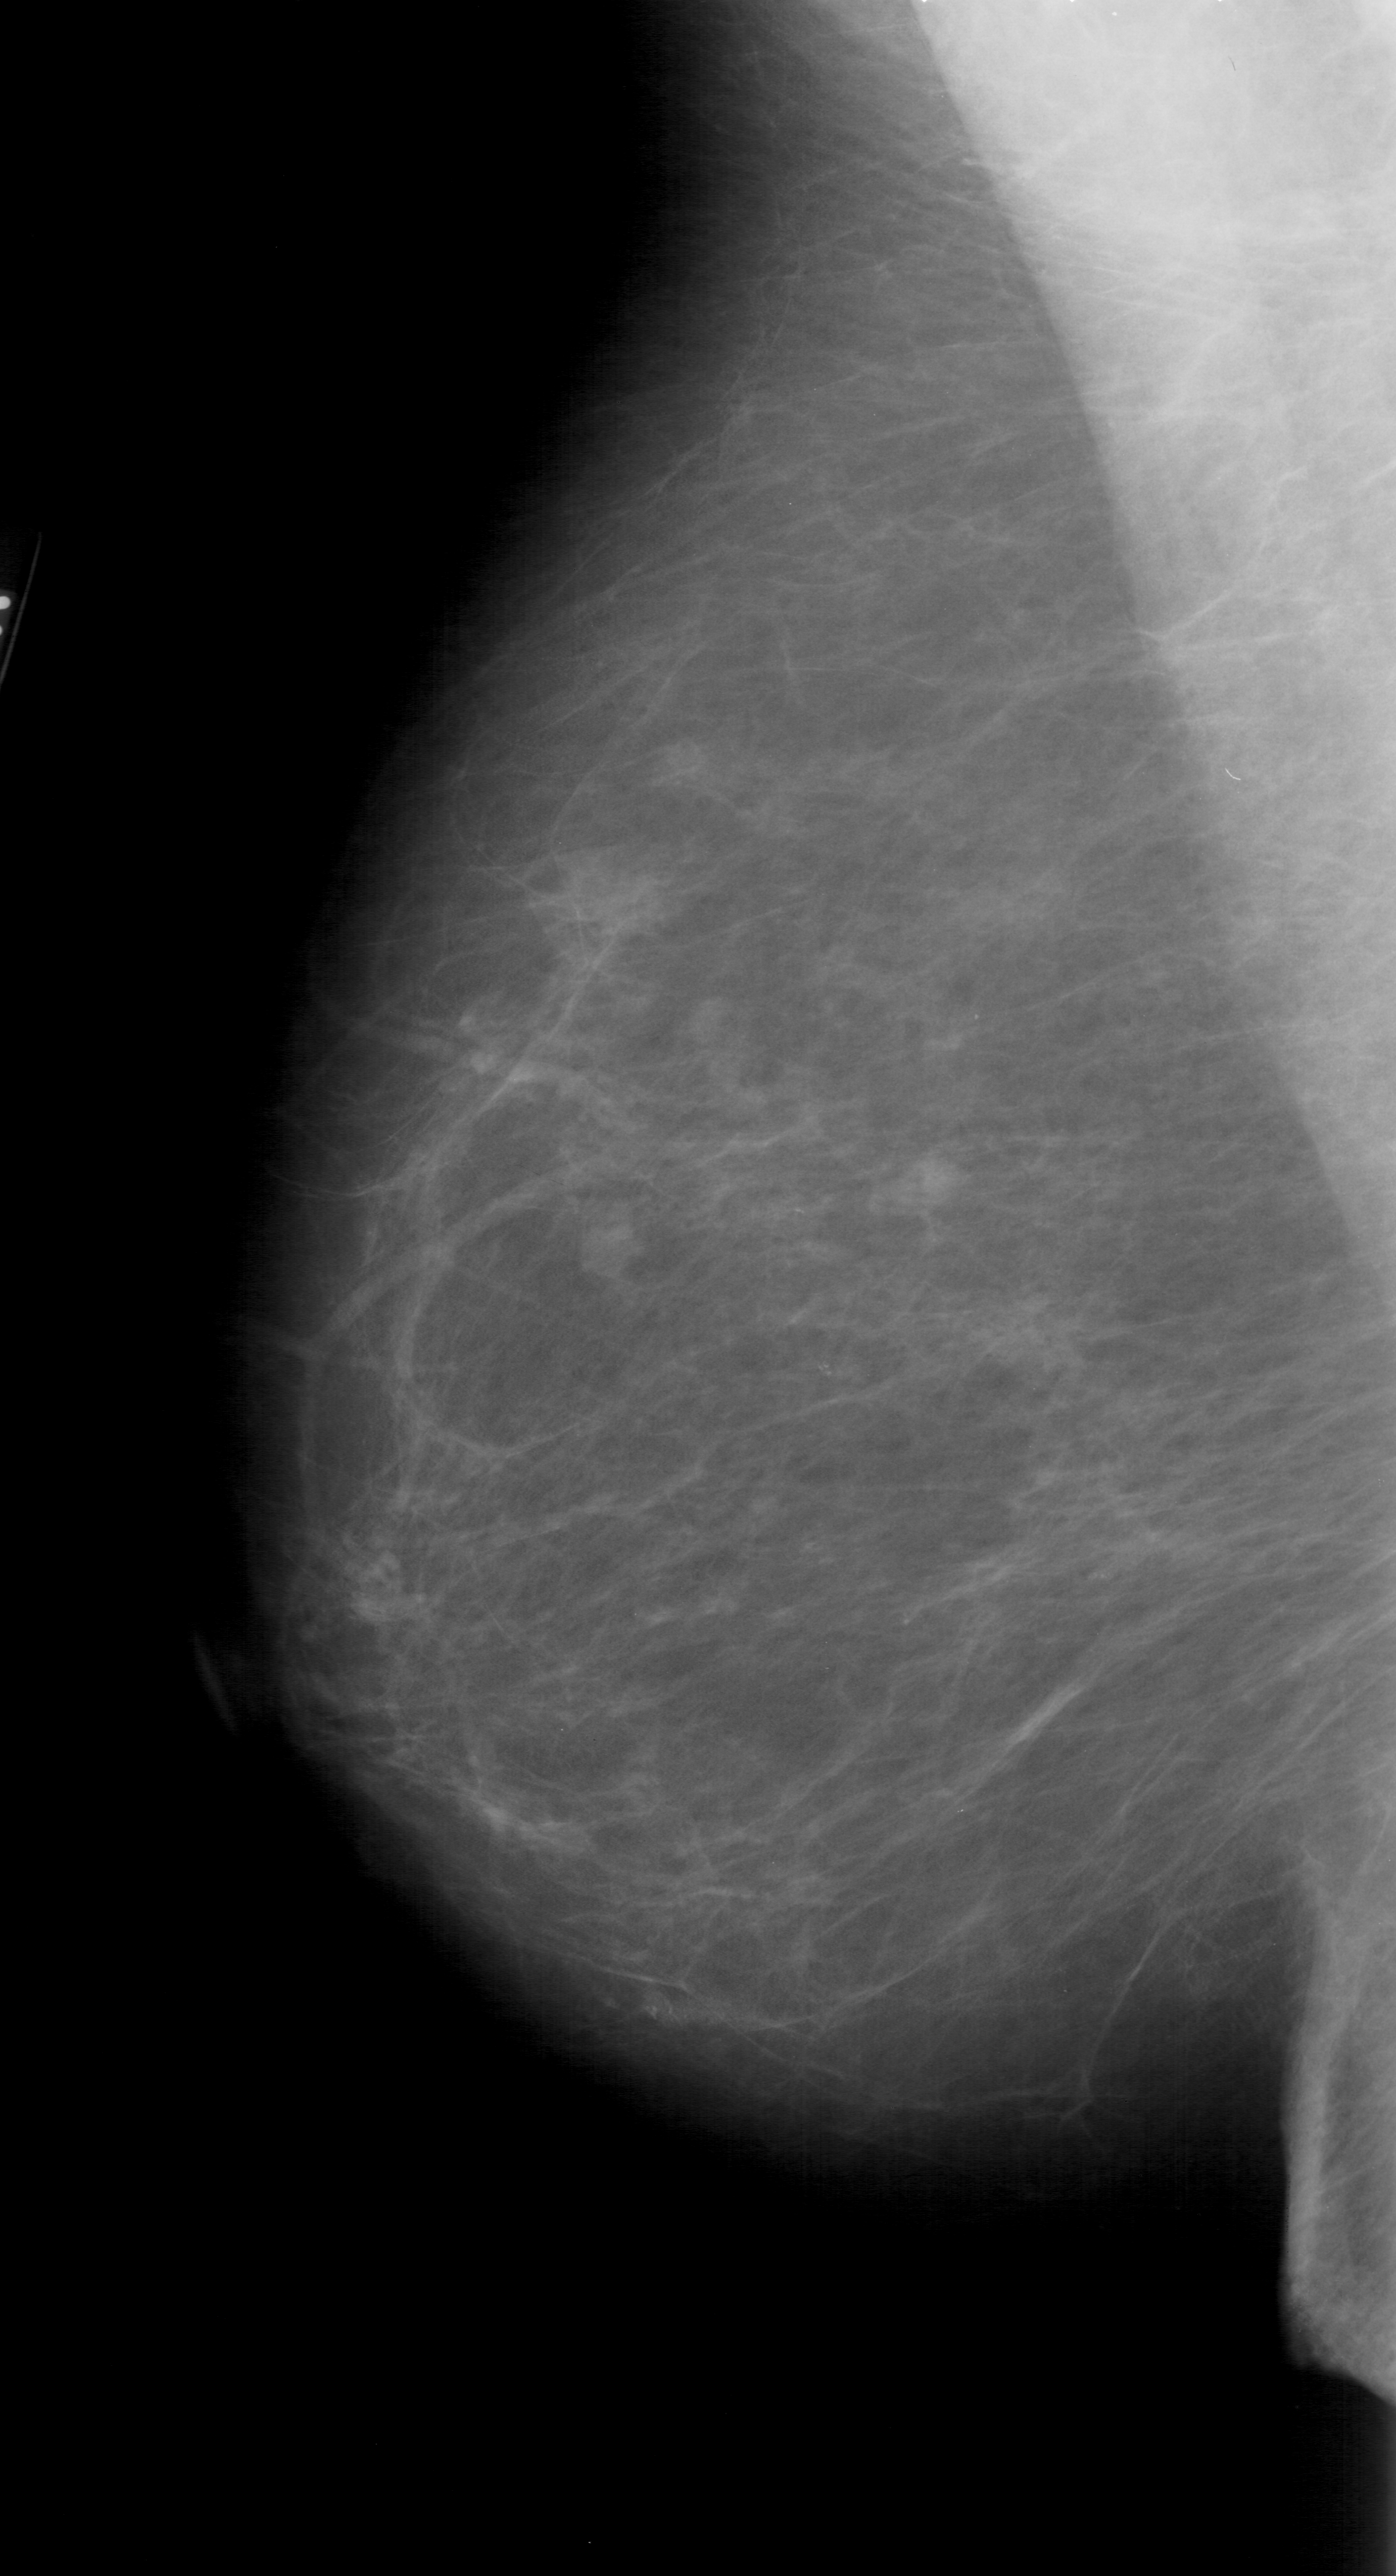
Mammogram (digitized film), left breast, mediolateral oblique (MLO) view, breast composition: scattered fibroglandular densities (BI-RADS density category 2 of 4).
Mass, shape lobulated, margins microlobulated; BI-RADS assessment category 4; pathology result (as recorded, not read from the image): benign.